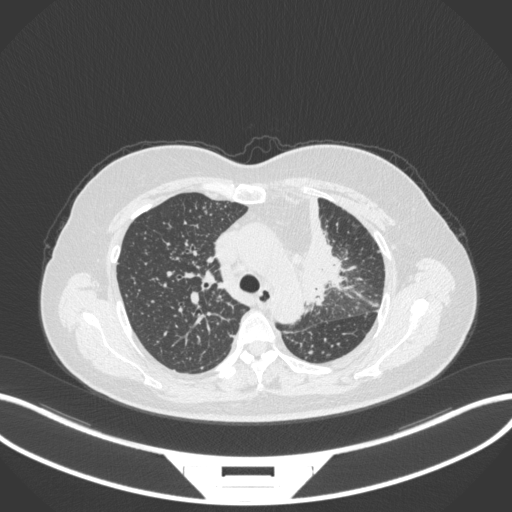
Chest CT, one axial slice; position 235 of 348 along the scan axis; 120 kVp; lung window (W 1500 / L -600 HU); 1 mm slice thickness; 512 × 512 image matrix. Female patient, age 49 years. From the clinical record (not read from this slice): clinical TNM (as recorded): T1c N0 M1.
Annotated regions visible in this slice (rectangle marked by the reading radiologist):
- lung tumour (recorded histology: adenocarcinoma): bounding box [x1, y1, x2, y2] px = [292, 186, 349, 312]